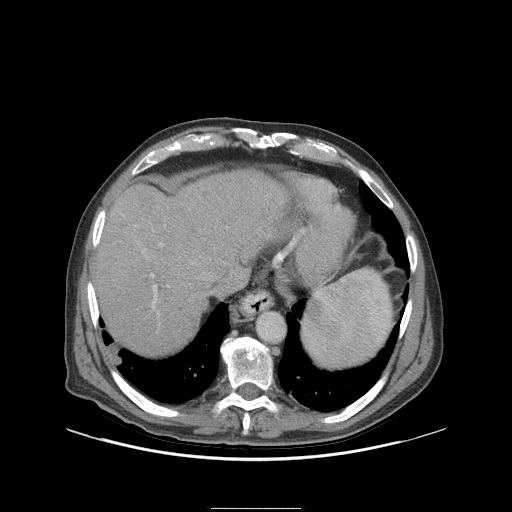
Contrast-enhanced abdominal CT (liver protocol), one axial slice; slice 82 of 105 in the series (ordered by position); reconstruction kernel STANDARD; soft-tissue window (W 400 / L 40 HU); 2.5 mm slice thickness; 512 × 512 image matrix, field of view 440 × 440 mm. From the clinical record (not read from this slice): diagnosis: hepatocellular carcinoma (patient treated with transarterial chemoembolisation; whether this scan precedes or follows treatment is not stated here); TNM stage (as recorded): Stage-I; Child-Pugh class: A; tumour nodularity: uninodular.
Structures marked on this image (semi-automatic segmentation, software-assisted and operator-edited):
- abdominal aorta: bounding box (x1, y1, x2, y2) in pixels: (257, 313, 285, 342)
- liver parenchyma outside the tumour (the mass and vessels are separate outlines, so this box may not span the whole liver): (92, 170, 288, 352)
- liver vessels: (151, 244, 162, 303)